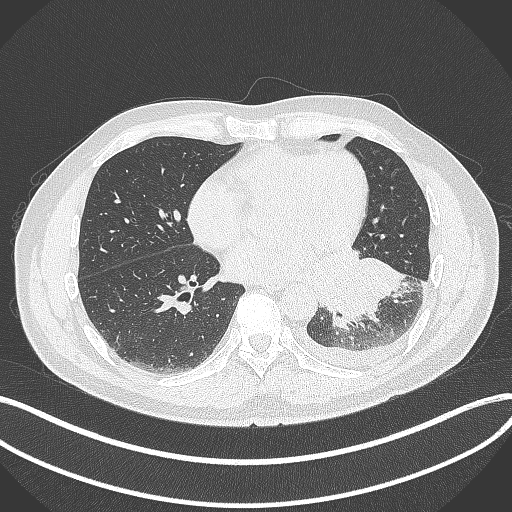
Chest CT, one axial slice; slice 146 of 342 in the series (ordered by position); reconstruction kernel B70f; 120 kVp; lung window (W 1500 / L -600 HU); 1 mm slice thickness; 512 × 512 image matrix. Patient: male, 58 years. Case-level facts recorded for this patient, not image findings: clinical TNM (as recorded): T3 N1 M1b.
Structures marked on this image (rectangle marked by the reading radiologist):
- lung tumour (recorded histology: small cell carcinoma): bounding box [x1, y1, x2, y2] px = [301, 245, 408, 325]